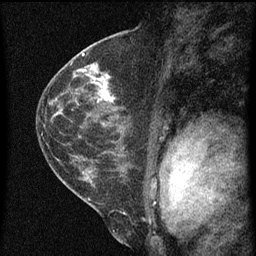
Breast MRI (dynamic contrast-enhanced), one sagittal slice; position 36 of 60 along the scan axis; dynamic contrast-enhanced series, image 2 of 3 at this slice position (ordered by acquisition); 1.5 T; TE 4.2 ms, TR 8 ms; 256 × 256 image matrix, field of view 180 × 180 mm. Patient: female, 48 years.
Annotated regions visible in this slice (semi-automatically segmented with operator editing):
- analysis volume of interest (the breast-tissue region the enhancement analysis was run in; not a lesion): box from (x=82, y=68) to (x=126, y=125) px
- tumour enhancement mask (voxels above the 70 % enhancement threshold inside the analysis volume of interest): (x=85, y=70)–(x=114, y=101)